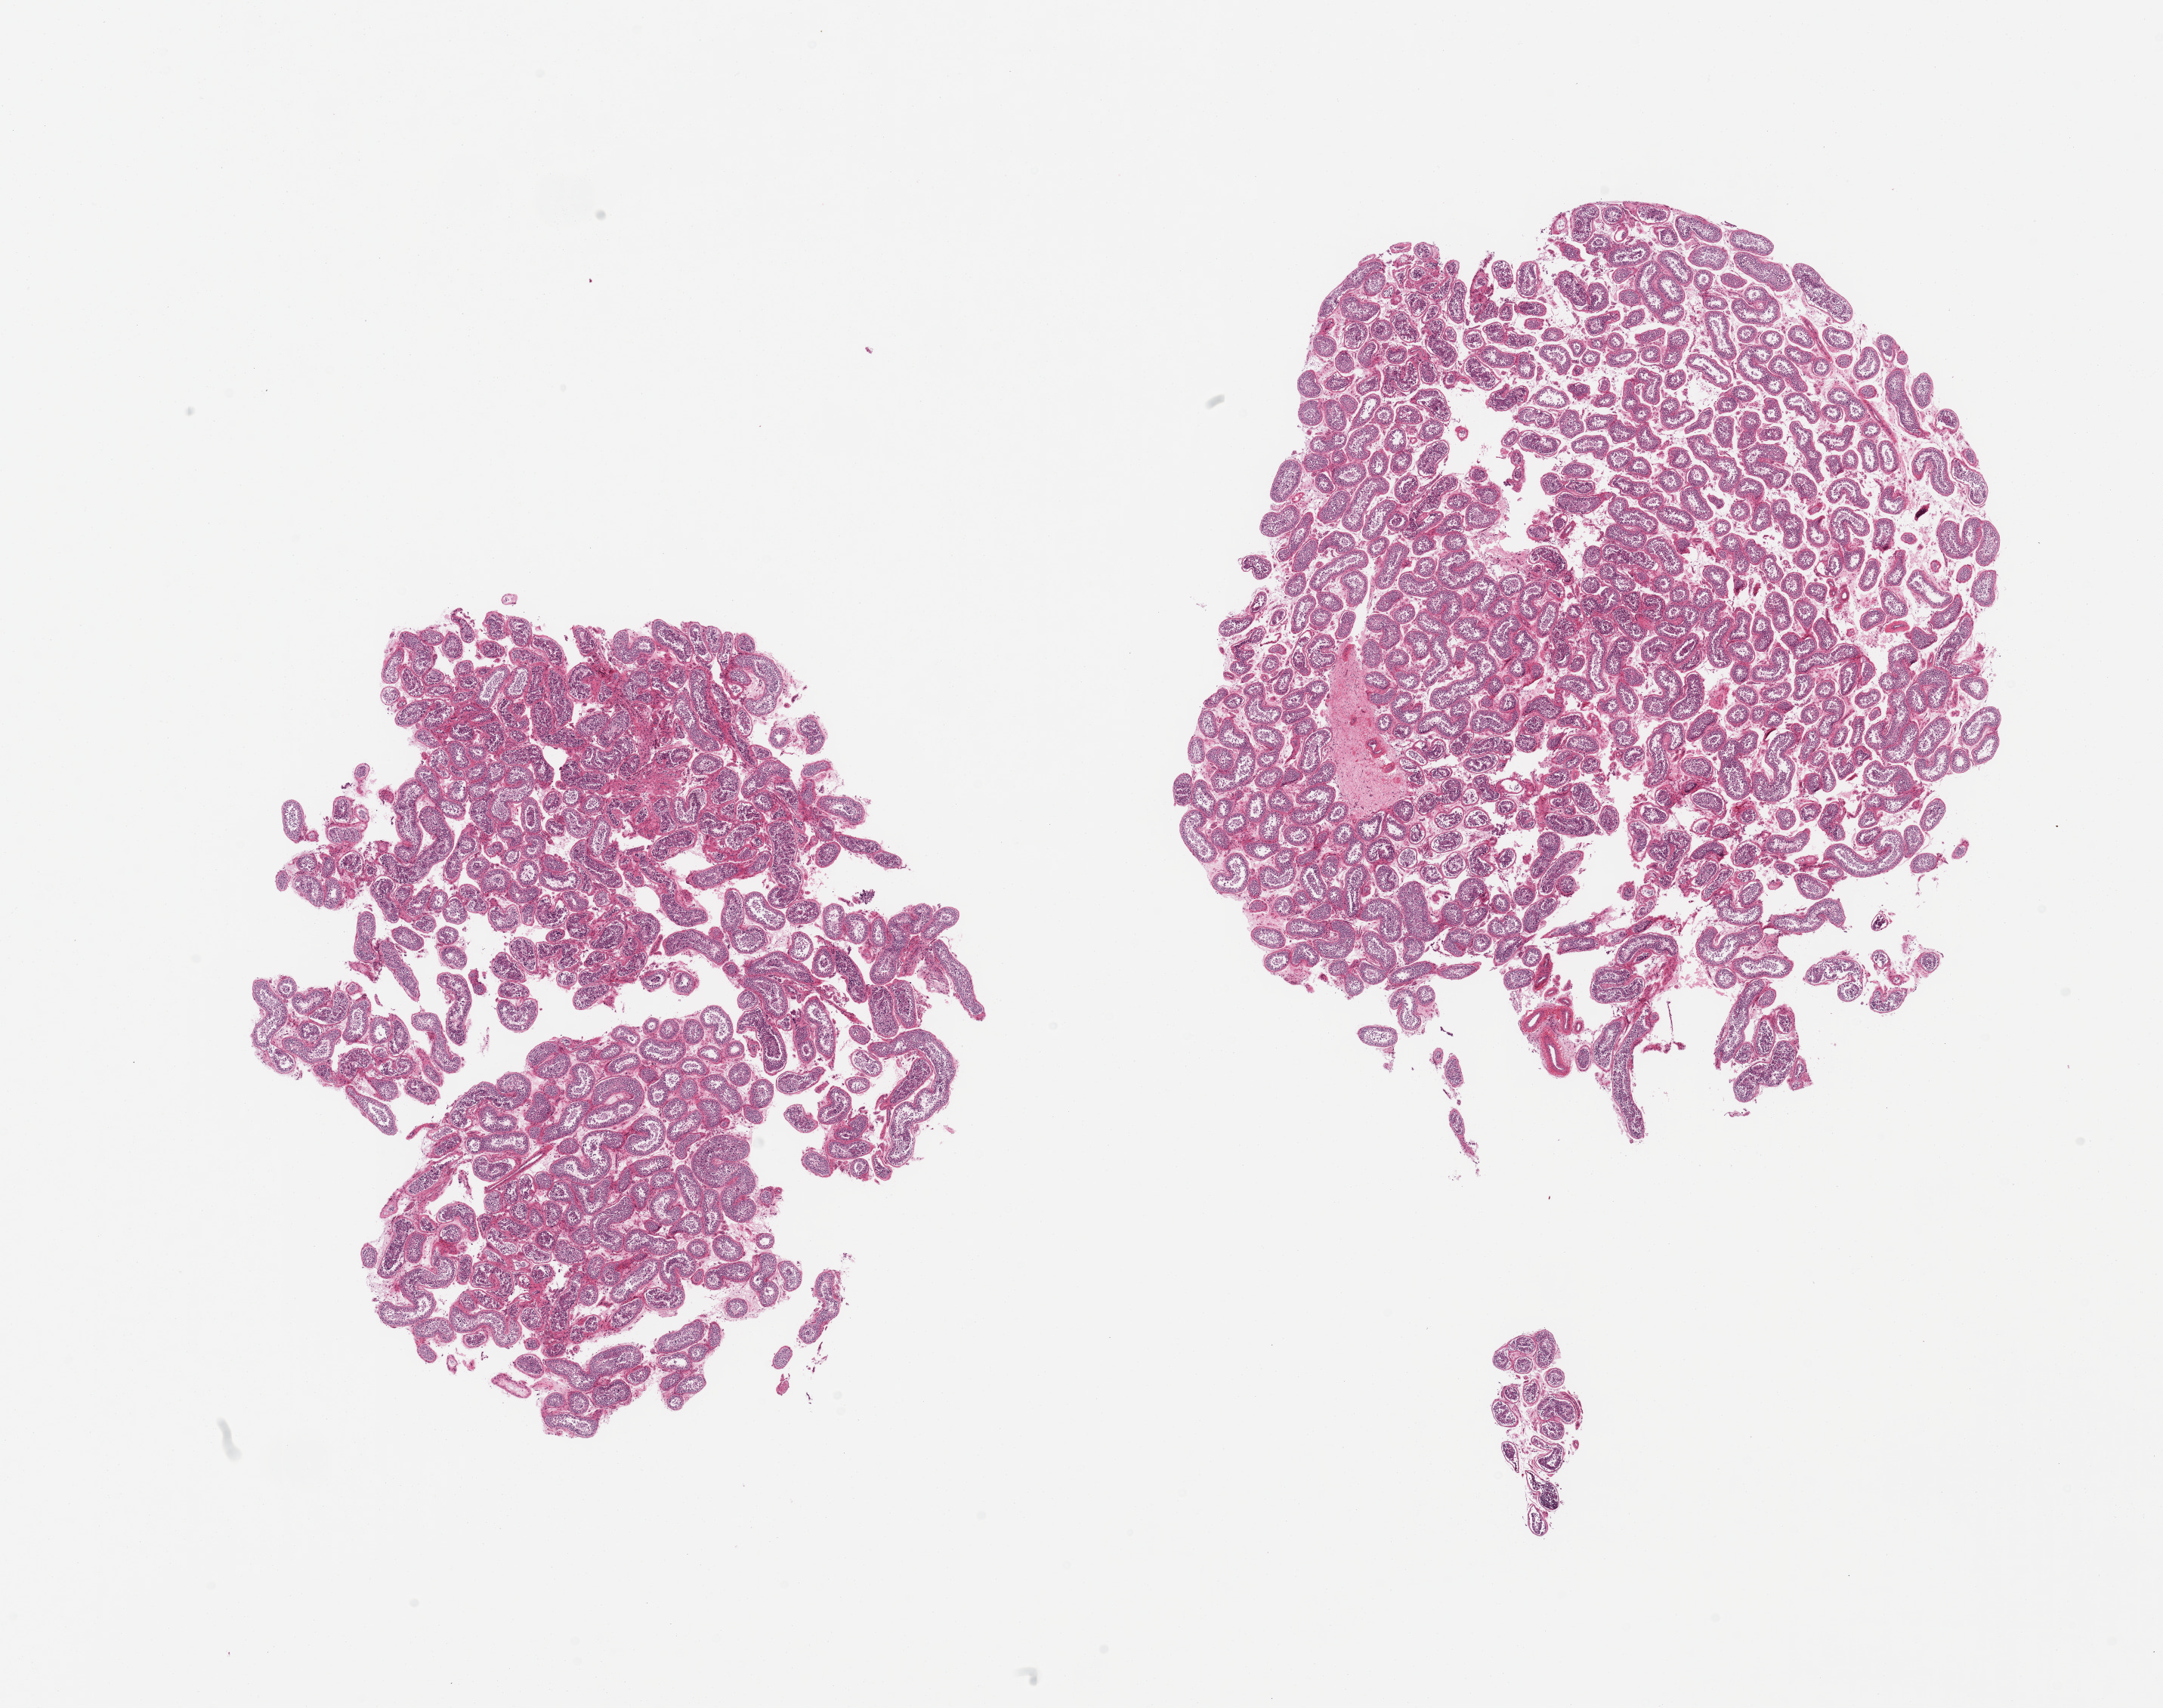
Digitized H&E-stained section, low-resolution overview of the scanned area, about 22.6 x 17.9 mm. PAXgene-fixed paraffin-embedded (PFPE) section. Sampled site (target tissue): testis. Donor tissue sample. Male donor.
Reviewer comment on this tissue sample: 2 pieces; spermatogenesis present.